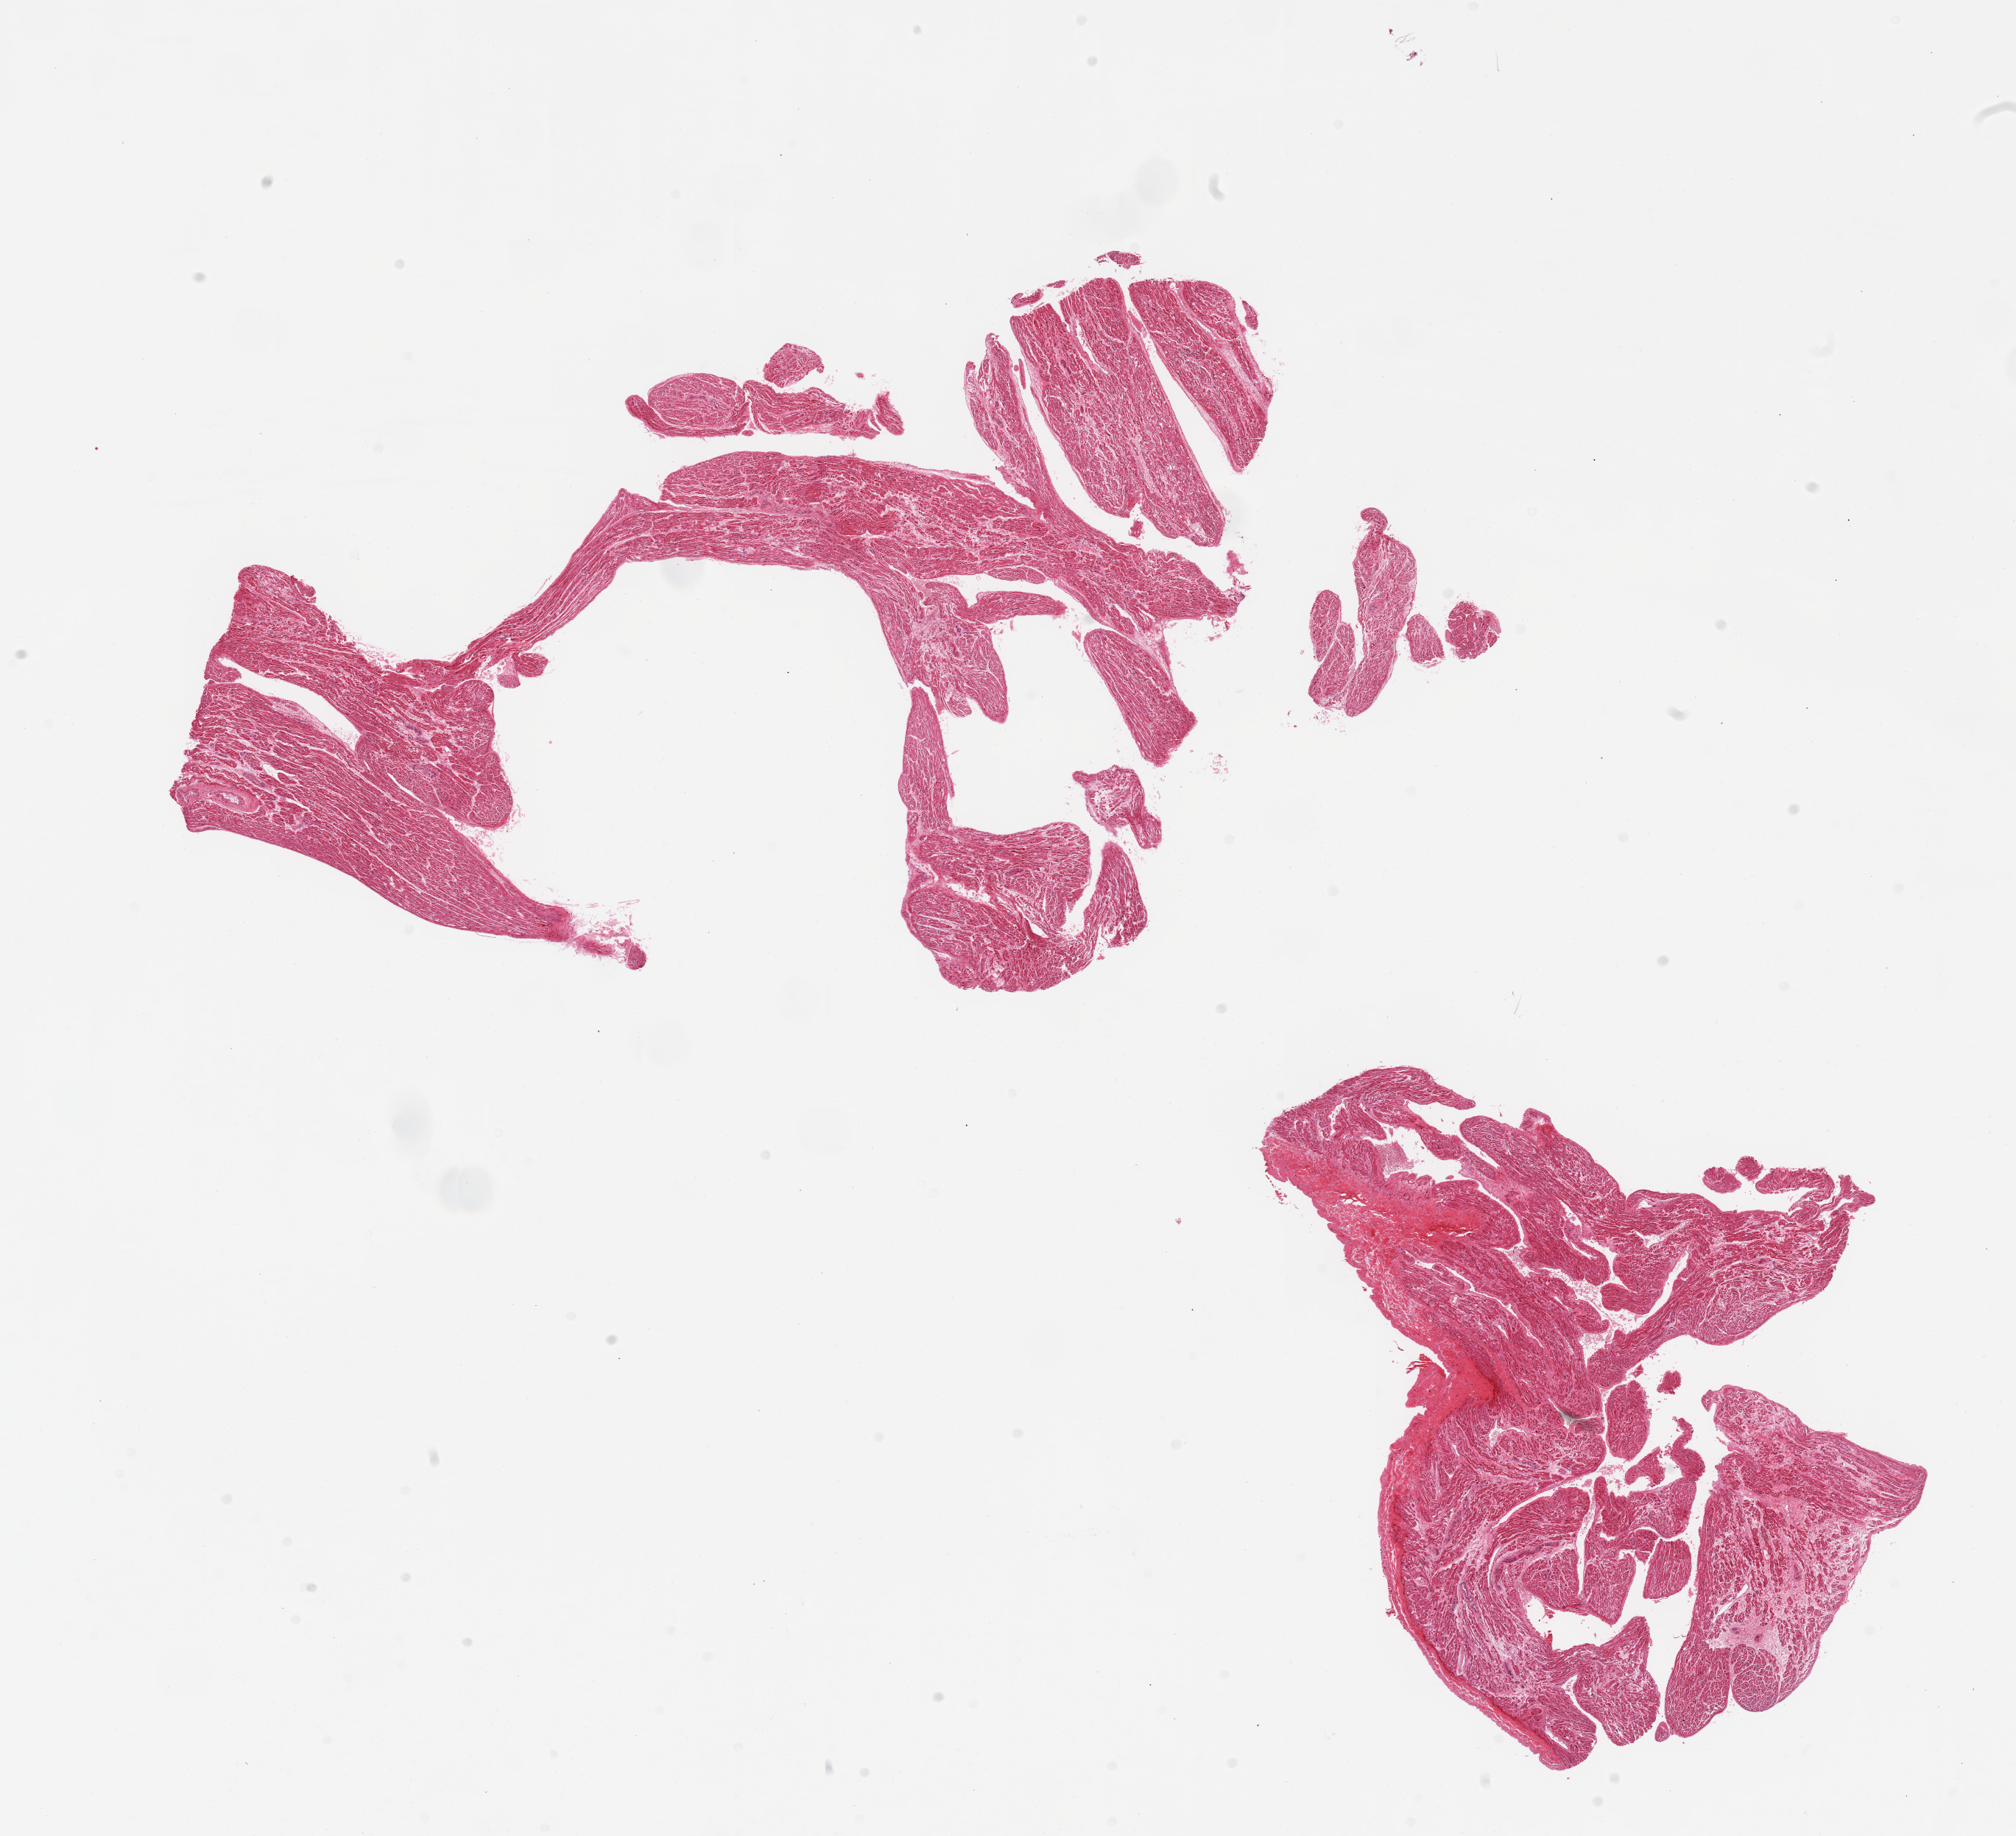
Whole-slide image, hematoxylin and eosin (H&E) stain — low-resolution overview of the scanned area, about 21.7 x 19.7 mm (slide scanned at 20x); PAXgene-fixed paraffin-embedded (PFPE) section; target tissue: auricular appendage; donor tissue sample. Male donor.
* review note (as recorded): 2 pieces